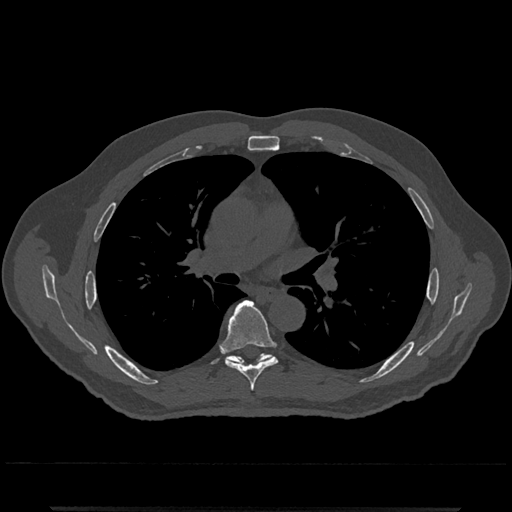
CT including the spine, one axial slice; 120 kVp; bone window (W 1800 / L 400 HU); 0.5 mm slice thickness; 512 × 512 image matrix, field of view 393 × 393 mm. Patient: male, 67 years. Case-level facts recorded for this patient, not image findings: primary cancer: prostate.
Outlined on this slice (semi-automatic segmentation, software-assisted and operator-edited):
- T6 vertebra: bounding box (x1, y1, x2, y2) in pixels: (221, 300, 278, 391)
- T7 vertebra: (227, 354, 271, 364)